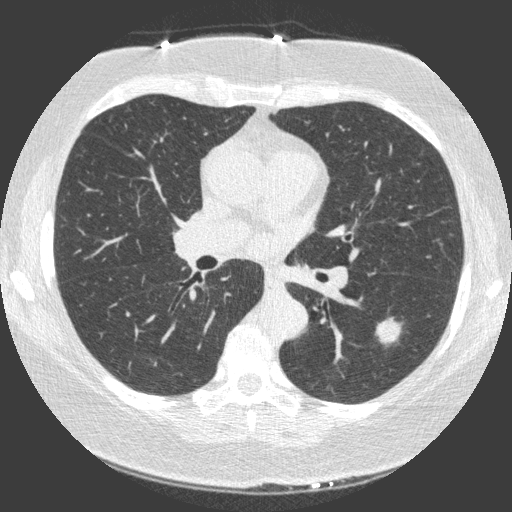
Chest CT (low-dose screening protocol), one axial image, third annual screen, lung window (W 1500 / L -600 HU), 1 mm slice thickness, standard (soft-tissue) reconstruction kernel (C), slice 61 of 149 in the series, 512 × 512 image matrix, field of view 330 × 330 mm. Female, age 66 years at enrolment. Current smoker at enrolment.
- Lesion marked by an expert reader, bounding box (x1, y1, x2, y2) in pixels: (365, 302, 420, 352).
- Reader record for this screening exam (exam-level; its link to the box is not recorded): non-calcified nodule or mass ≥4 mm, left lower lobe, 23 × 17 mm, spiculated (stellate) margins, soft tissue attenuation, pre-existing on the prior screen: yes; interval growth: yes.
- Official screen result: positive, other.
- Participant outcome: lung cancer diagnosed 15 days after this screen — non-small cell carcinoma, left lower lobe, poorly differentiated (G3), stage IA (AJCC 6th edition), 20 mm at pathology.